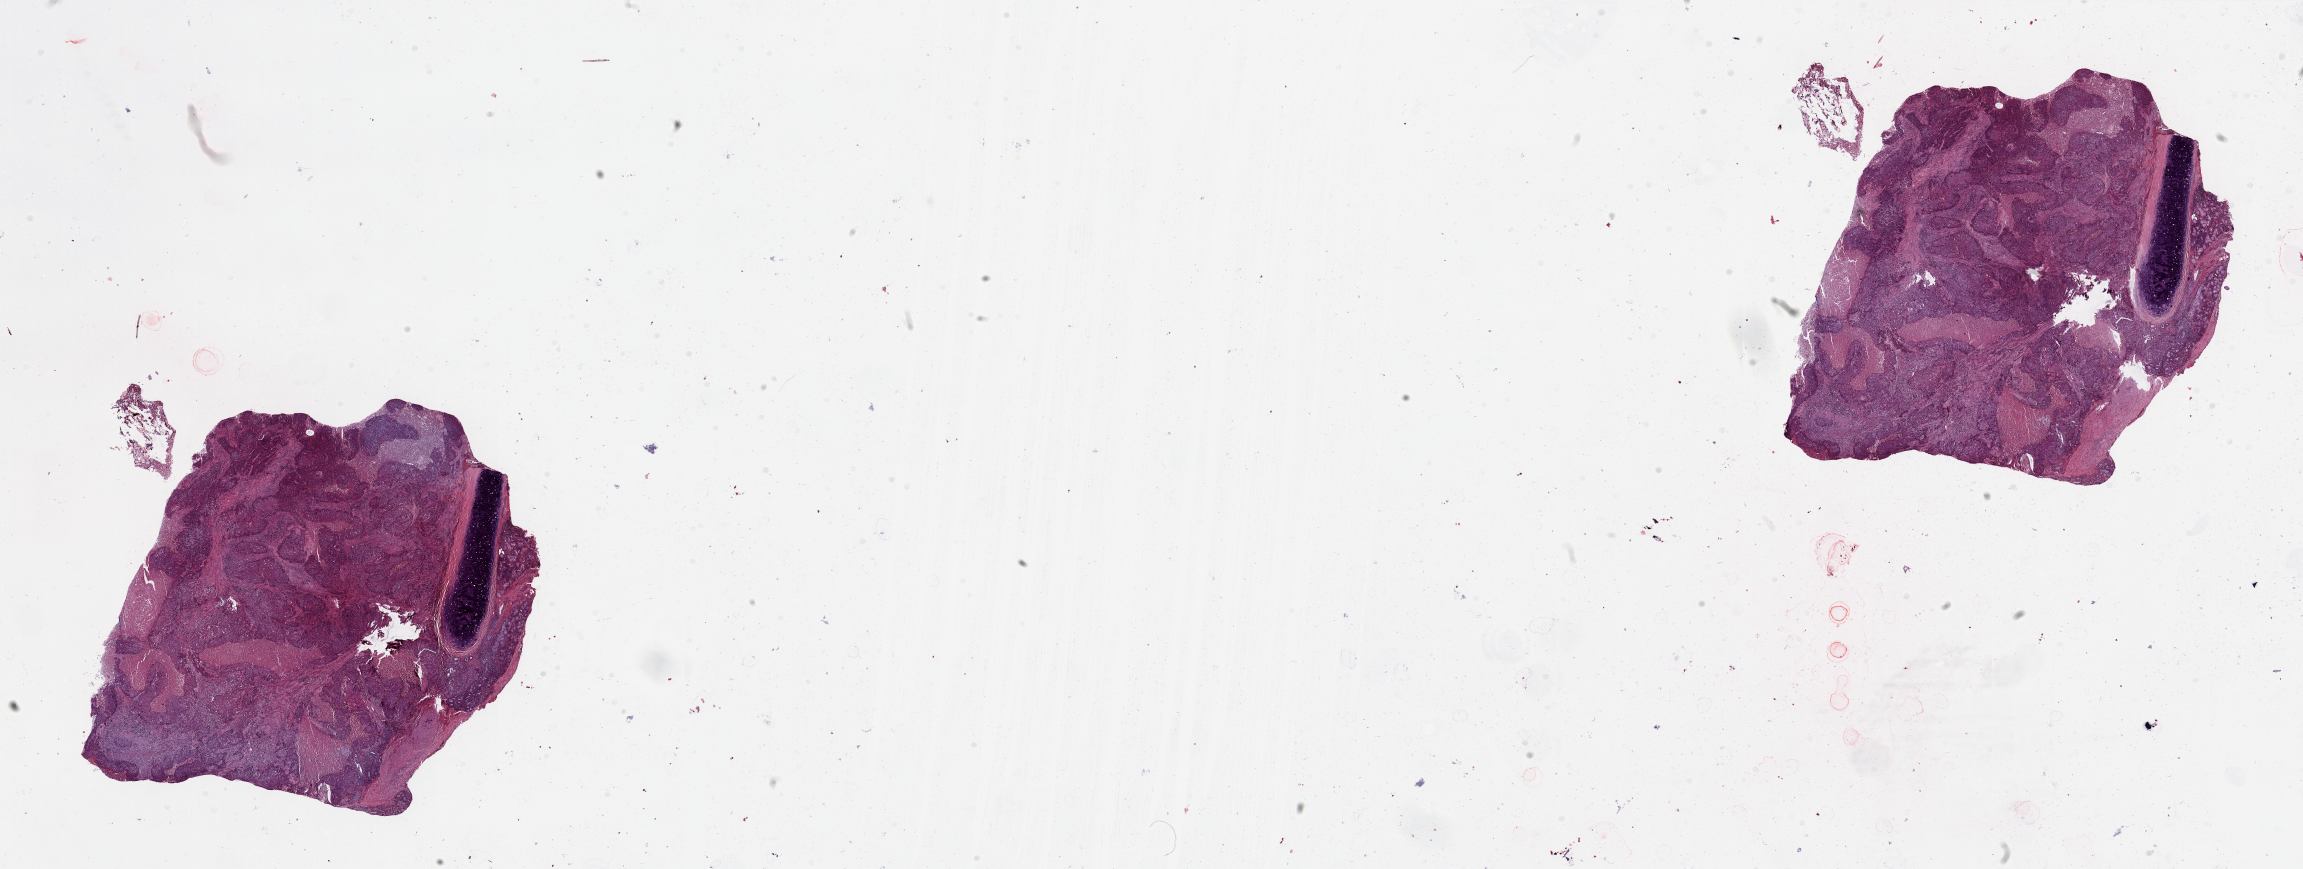
Whole-slide histology image, Hematoxylin and eosin (H&E) stained — shown as a low-resolution overview of the whole scanned area (about 36.4 x 13.7 mm, slide scanned at 20x), tumour tissue sample, lung. Patient: male, age 57 years. Histologic grade: G2 (moderately differentiated).
Primary tumour site (as recorded): left upper lobe. Diagnosis: Squamous cell carcinoma, NOS. AJCC pathologic stage: IIA.